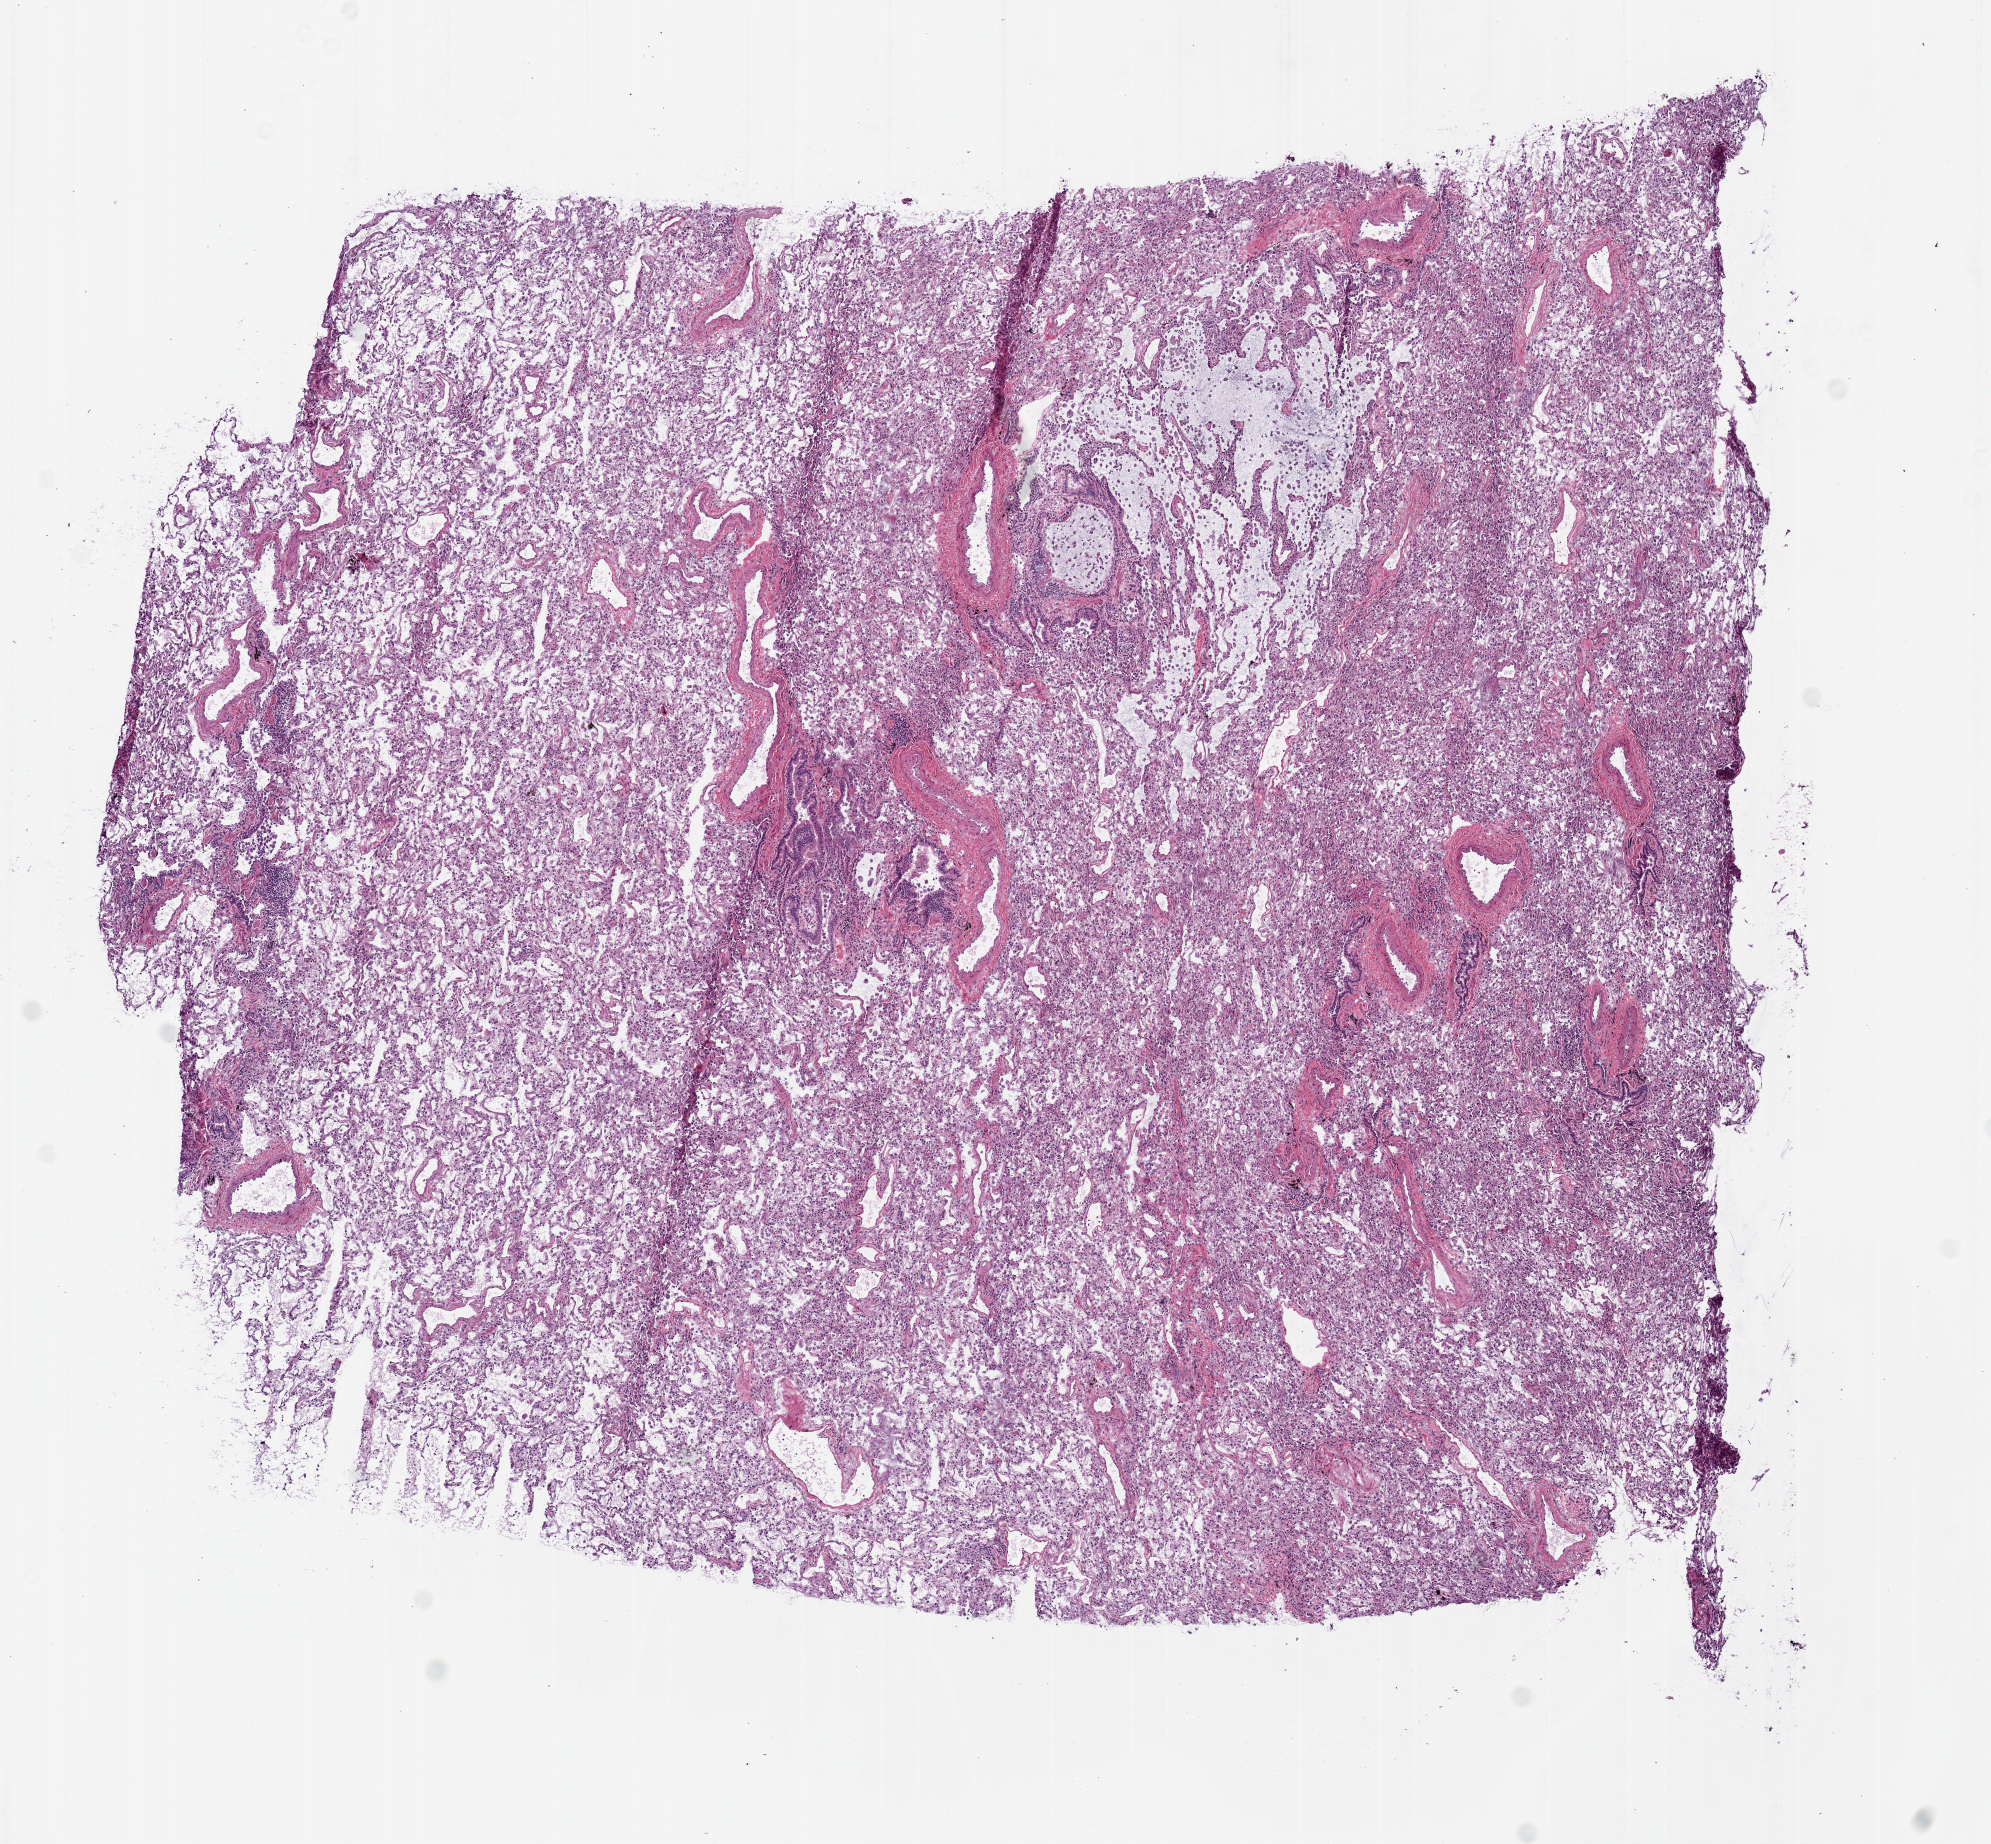
H&E whole-slide image — shown as a low-resolution overview of the whole scanned area (about 7.9 x 7.3 mm); frozen section from the top of the tissue portion; solid tissue normal (non-tumour tissue) sample from the lung. Male patient; age at initial diagnosis 81 years.
This section: solid tissue normal (non-tumour) sample from the same patient. Patient diagnosis: Adenocarcinoma, NOS (middle lobe, lung).